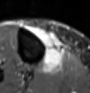
MRI of an extremity soft-tissue mass, one axial slice. Slice 29 of 60 in the series (ordered by position). STIR. MR volume resampled by the dataset authors to the PET/CT grid (not the native acquisition matrix). 3.27 mm slice thickness. 90 × 93 image matrix, field of view 88 × 91 mm. Female patient. From the clinical record (not read from this slice): histological type: undifferentiated – high grade; grade: high; site of the primary tumour: right thigh.
Annotated regions visible in this slice (expert contour drawn on MRI and transferred to this co-registered scan by the dataset authors):
- gross tumour volume (mass): bounding box (x1, y1, x2, y2) in pixels: (35, 30, 63, 73)